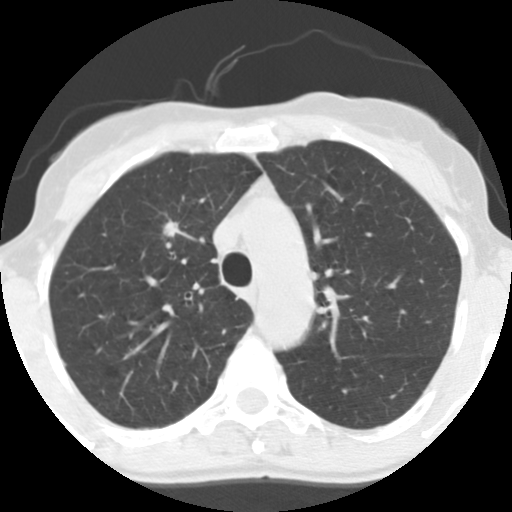
Axial slice from a low-dose chest CT screening exam; baseline annual screen; lung window (W 1500 / L -600 HU); 2.5 mm slice thickness; standard (soft-tissue) reconstruction kernel (STANDARD); slice 42 of 130 in the series. Female, age 56 years at enrolment.
Expert-annotated lung lesion, bounding box [x1, y1, x2, y2] px = [151, 211, 190, 250]. Reader record for this screening exam (exam-level; its link to the box is not recorded): non-calcified nodule or mass ≥4 mm, right upper lobe, 12 × 9 mm, spiculated (stellate) margins, soft tissue attenuation. Official screen result: positive, change unspecified: nodule(s) >= 4 mm or enlarging nodule(s), mass(es), or other non-specific abnormalities suspicious for lung cancer. Participant outcome: lung cancer diagnosed 779 days after this screen — adenocarcinoma, NOS, right upper lobe, moderately differentiated (G2), stage IA (AJCC 6th edition), 19 mm at pathology.